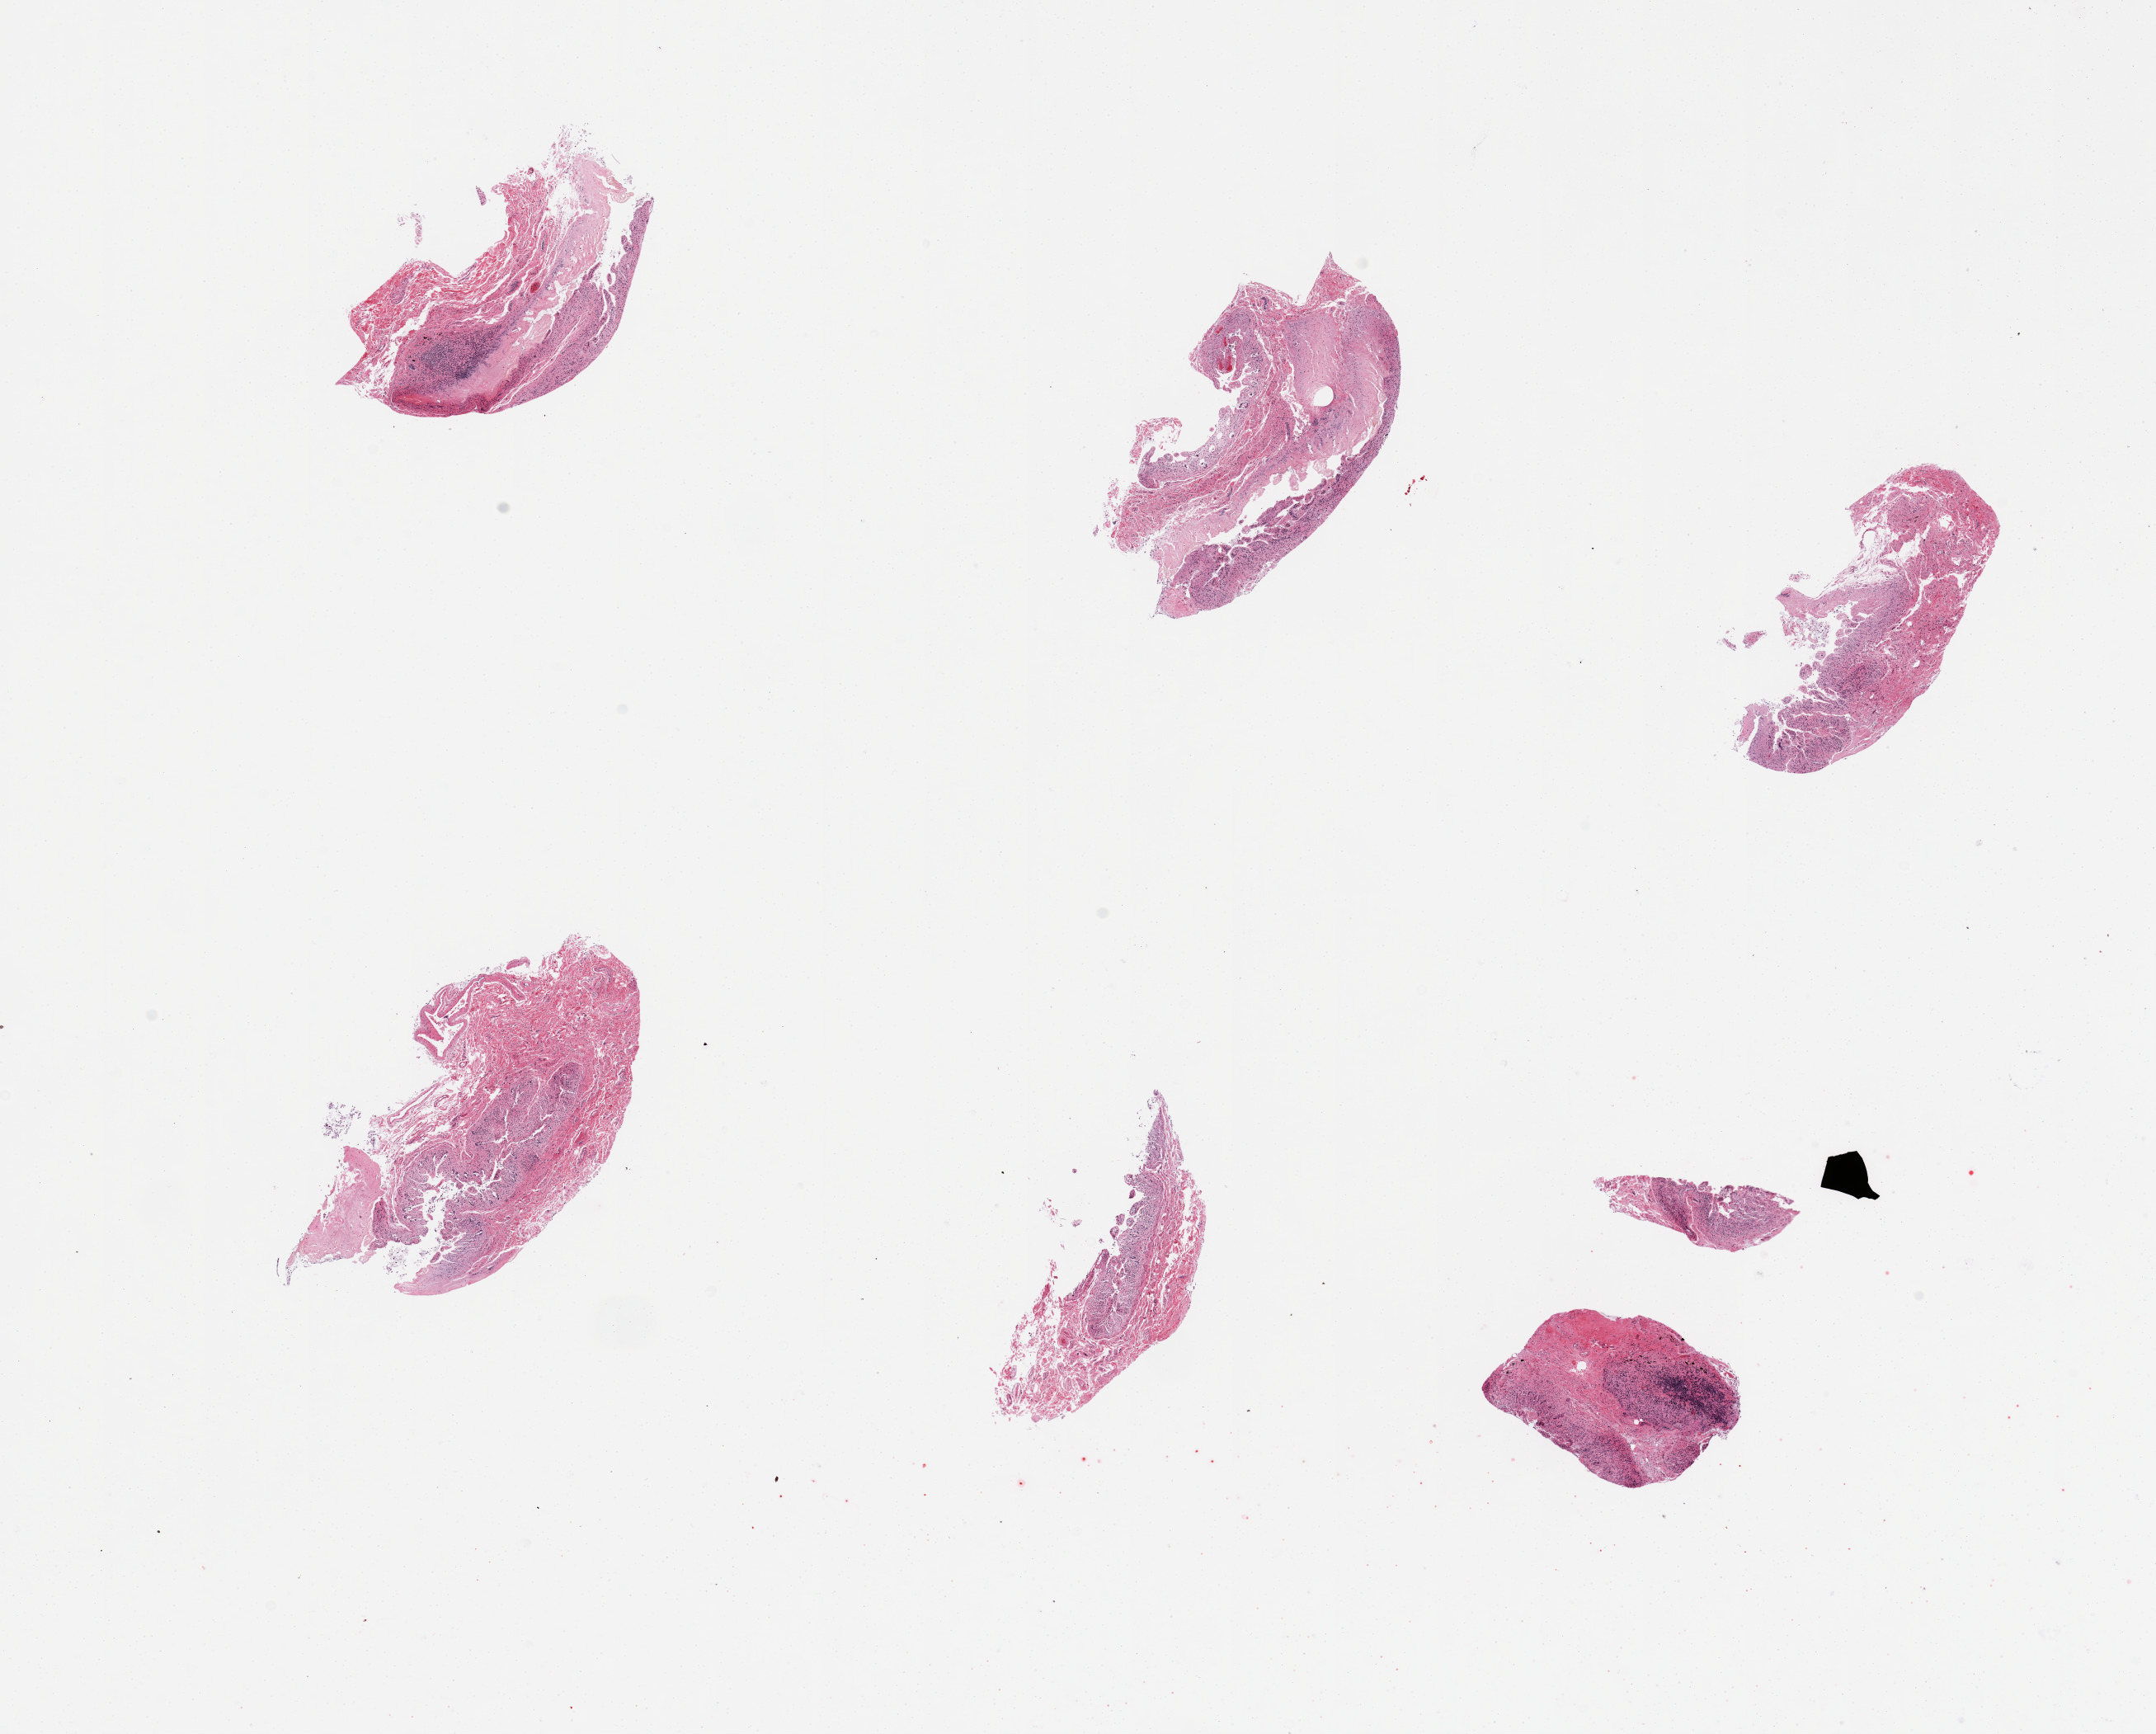
Whole-slide image, haematoxylin and eosin stain — low-resolution overview of the scanned area, about 20.7 x 16.6 mm (acquisition: 20x scan), PAXgene-fixed paraffin-embedded (PFPE) section, section of ileum (target tissue), donor tissue sample. Donor: female.
Reviewer comment on this tissue sample: 6 pieces; too autolyzed & too little lymphoid tissue.